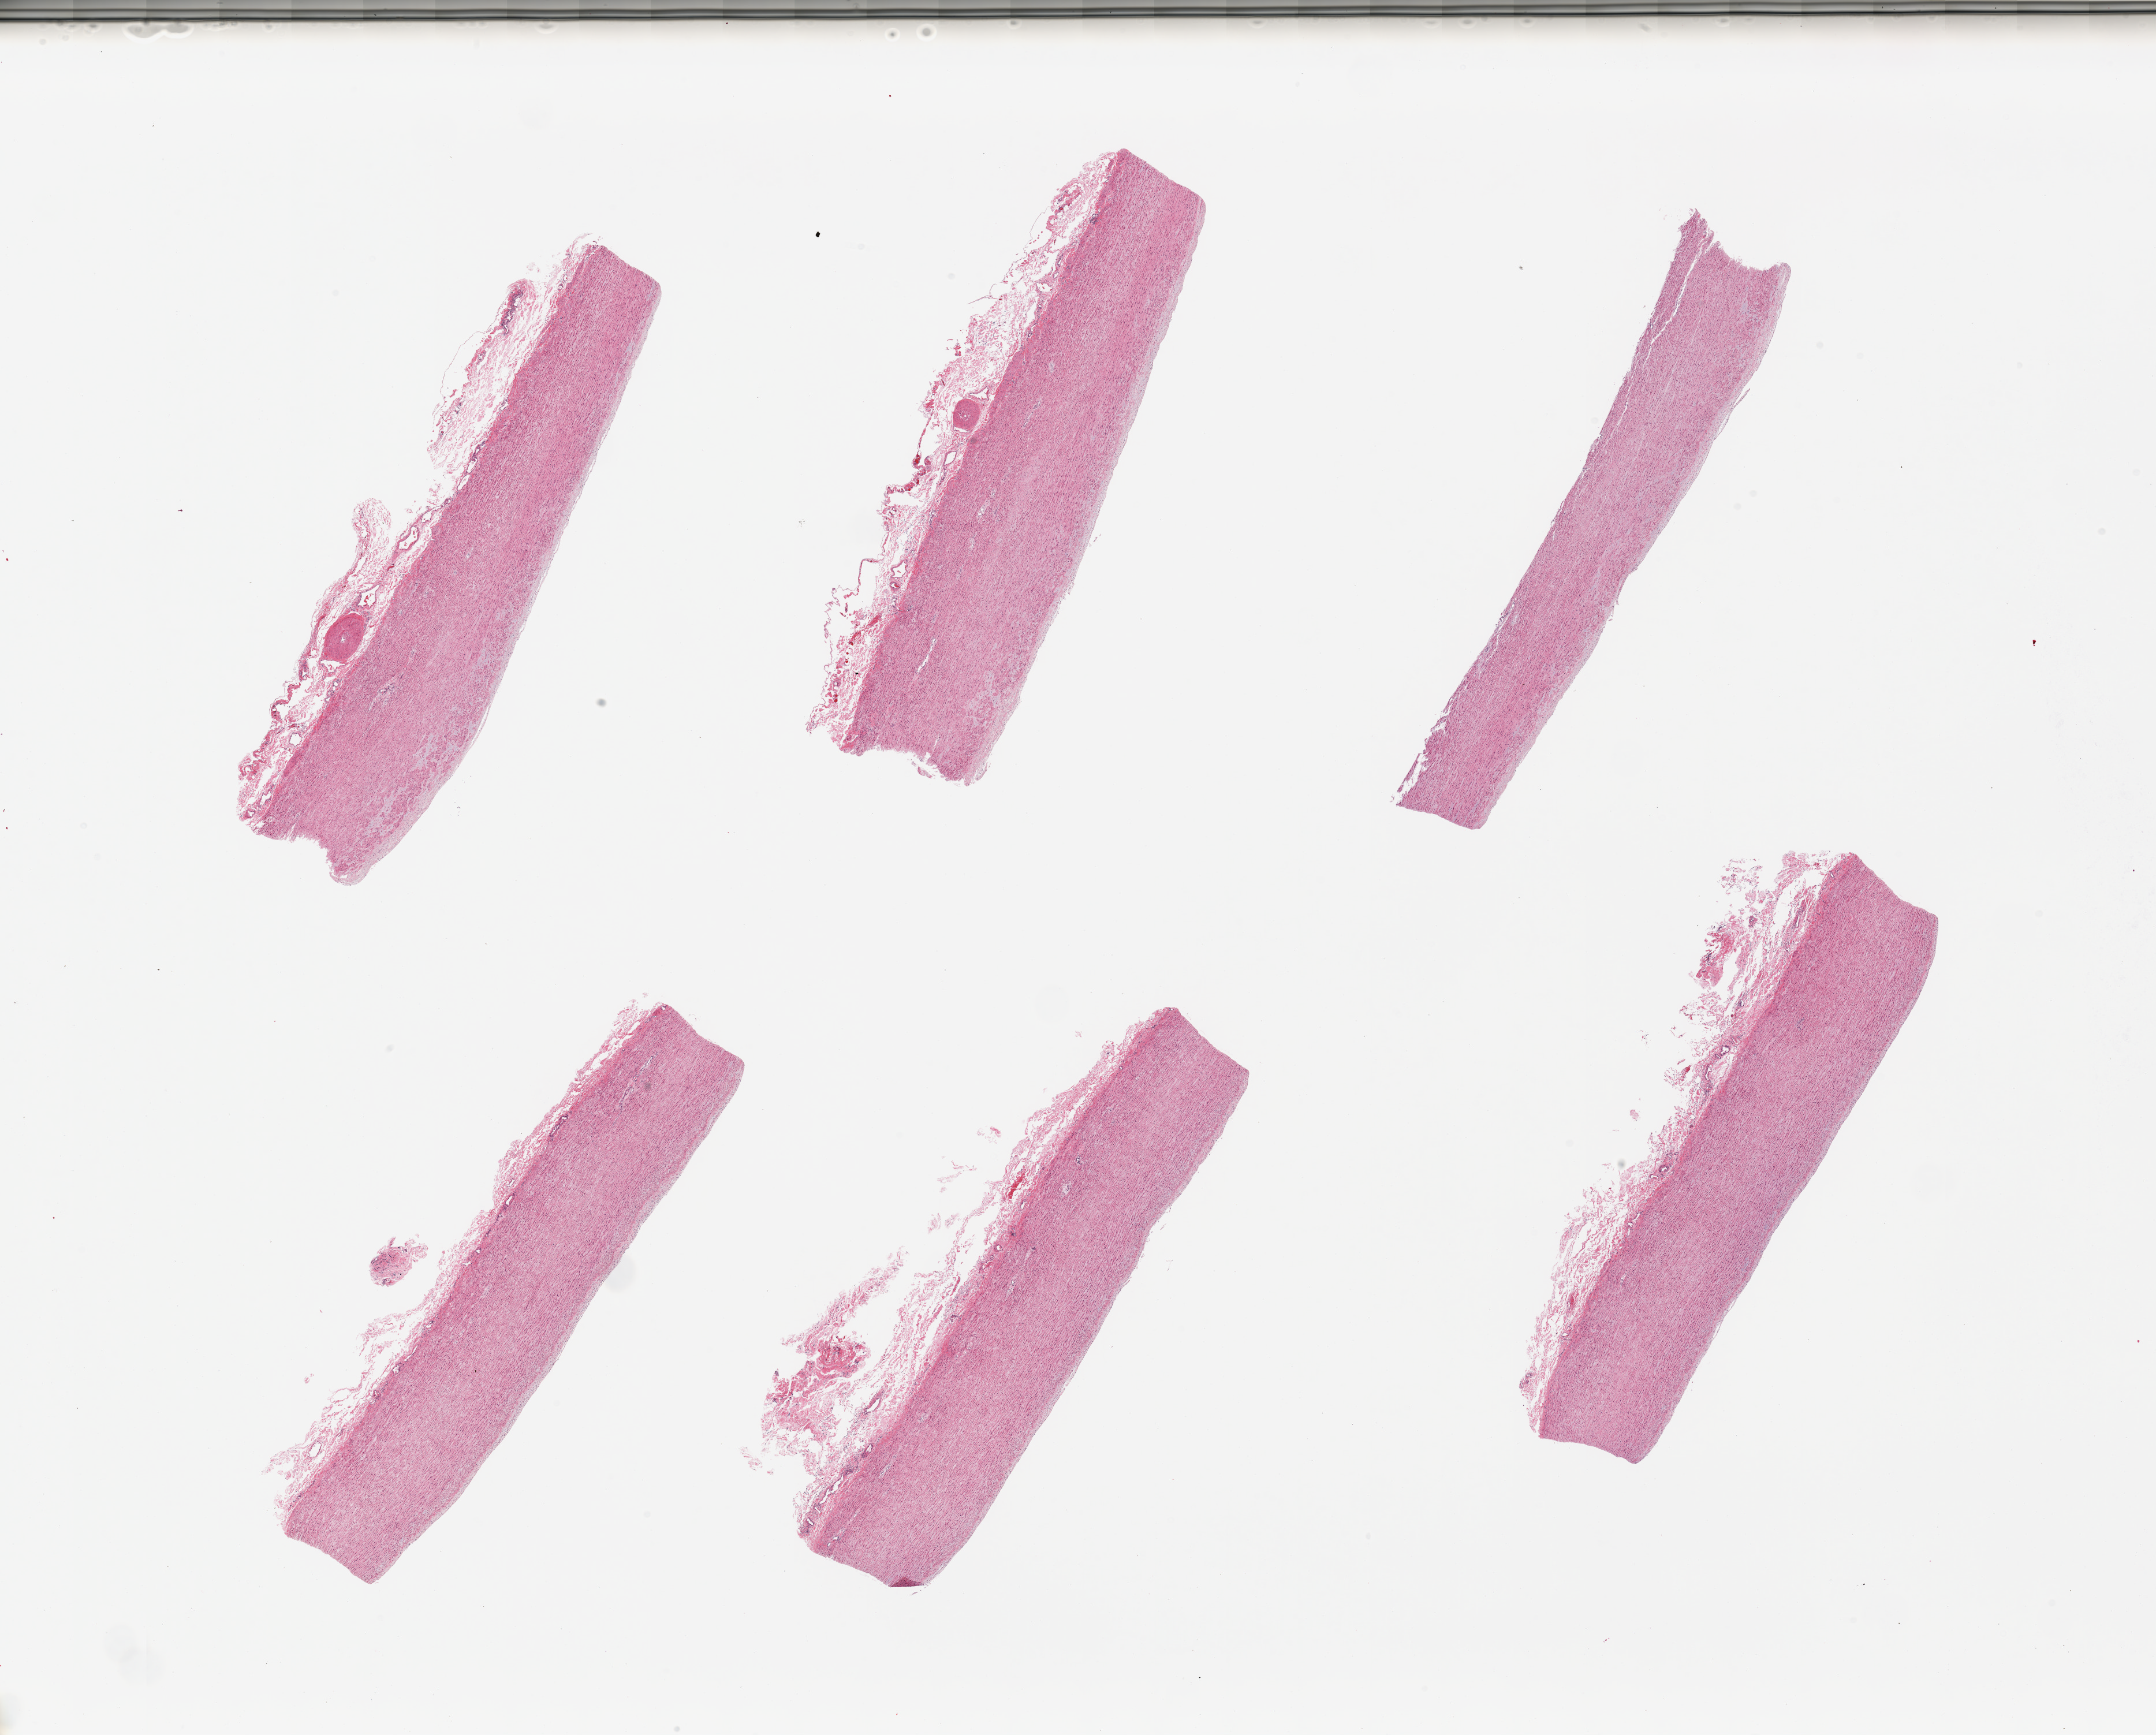
Haematoxylin and eosin whole-slide image, brightfield, a low-resolution overview of the entire scanned area, about 29.5 x 23.8 mm. PAXgene-fixed, paraffin-embedded tissue. Section of aorta (target tissue). Tissue donor sample. Female donor.
* review note (as recorded): 6 pieces; early plaque formation